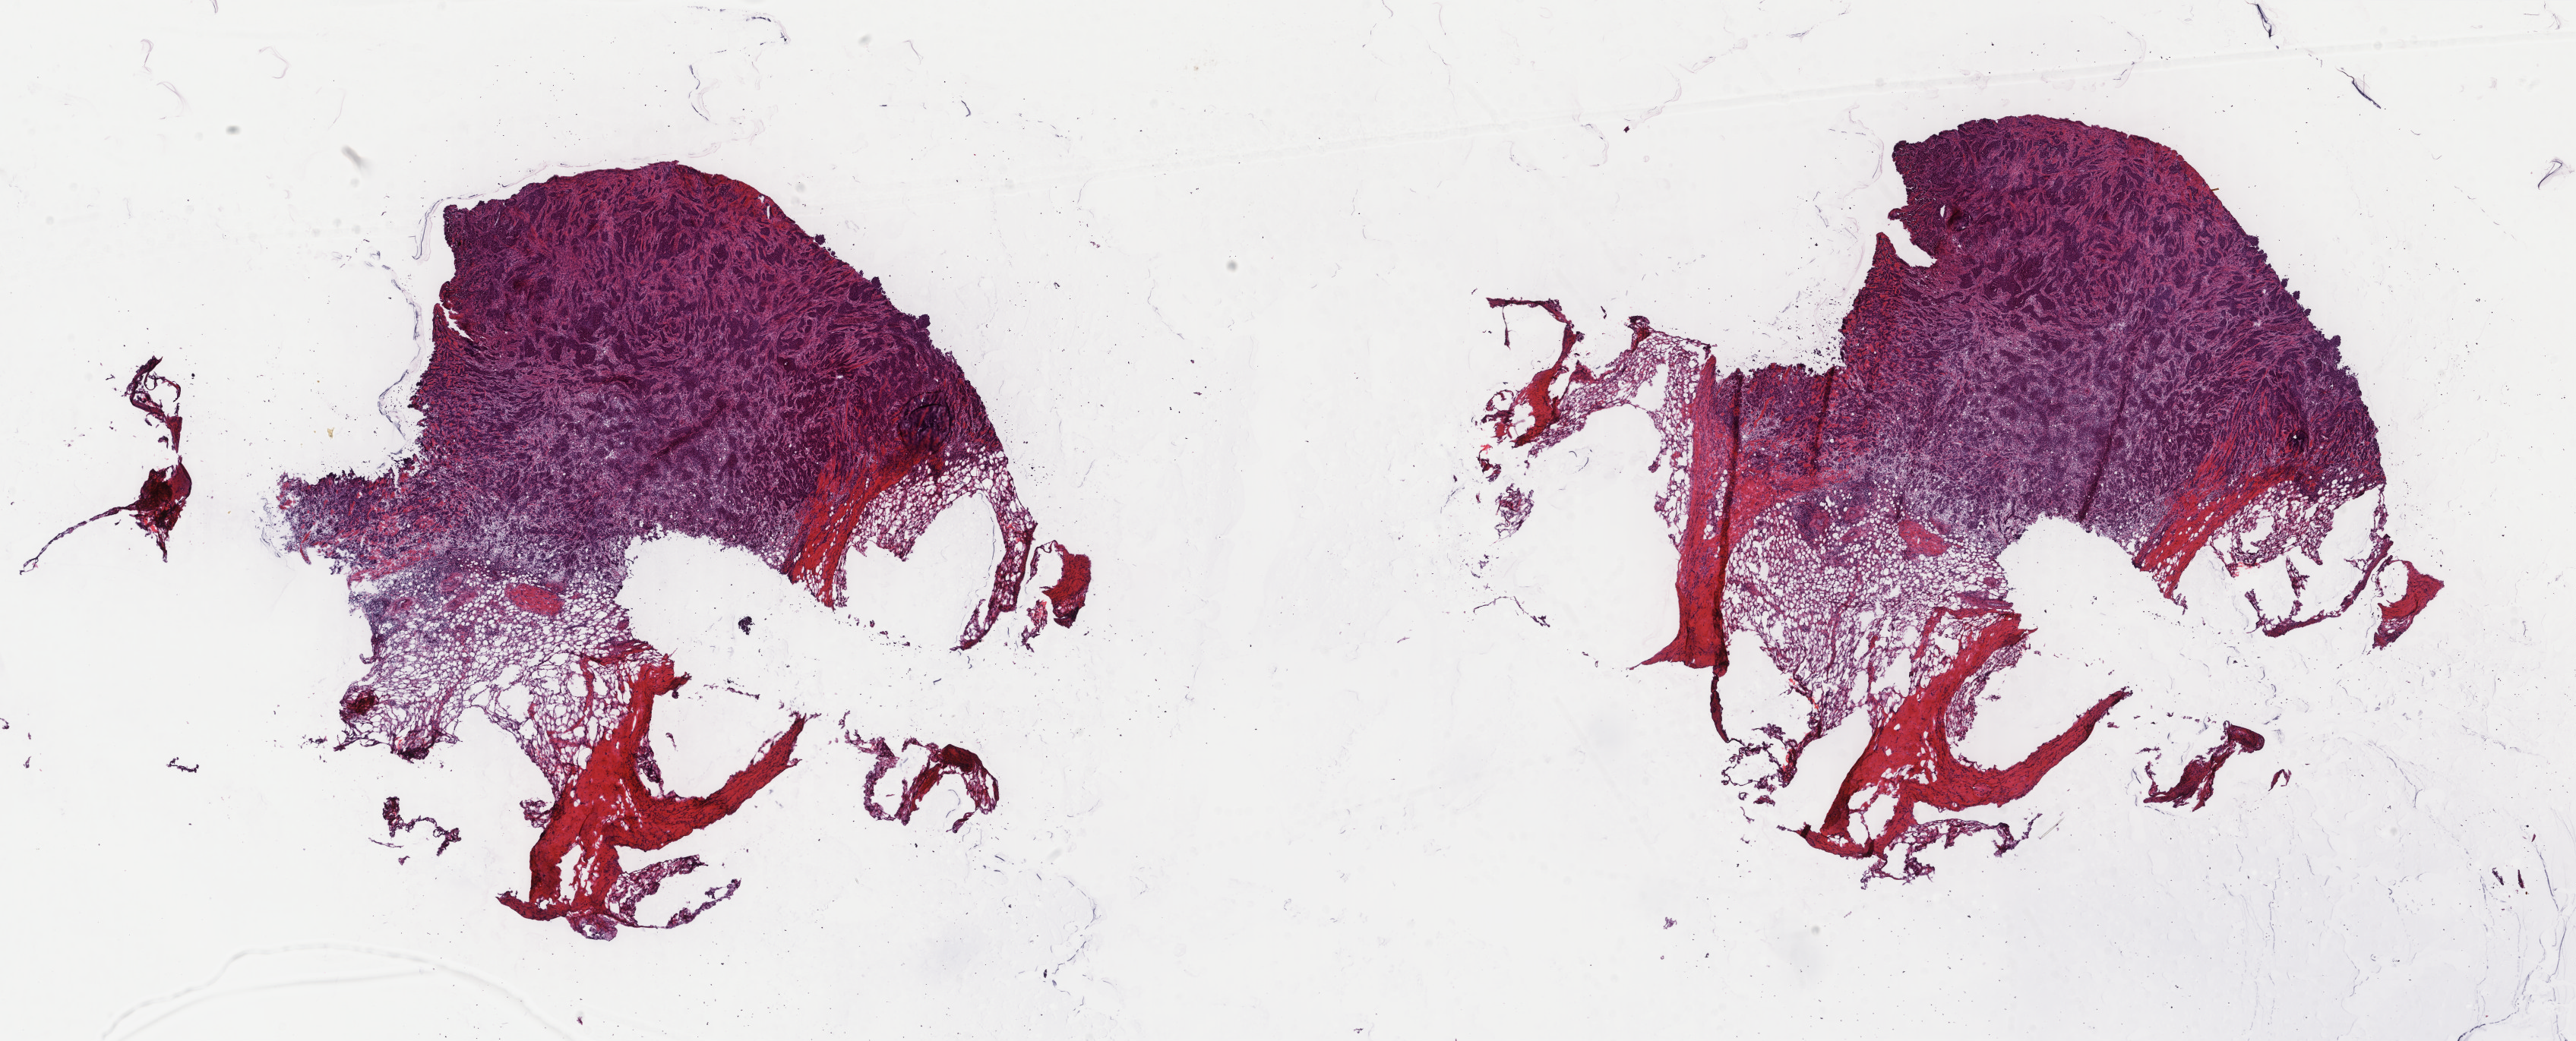
Whole-slide histology image, H&E — low-resolution overview of the scanned area, about 26.9 x 10.9 mm (slide scanned at 40x). Frozen section. Sample: primary tumour, breast. Female, age 46 years at initial diagnosis. Composition of this section per pathologist review: tumour cells 75%, tumour nuclei 80%, normal cells 0%, stromal cells 25%, necrosis 0%. Infiltration values recorded for this section: lymphocyte infiltration 0%, monocyte infiltration 0%, neutrophil infiltration 0%.
AJCC pathologic stage: IIA. TNM: T2 N0 M0. Lymph nodes positive (case pathology): 0 of 5 examined. Pathologic diagnosis: Infiltrating duct carcinoma, NOS.